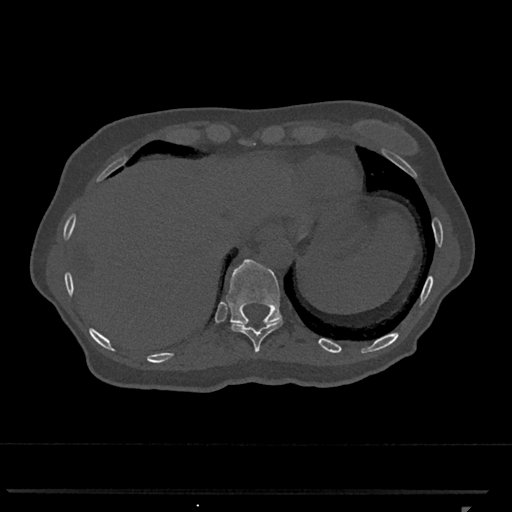
CT including the spine, one axial slice. Slice 545 of 793 in the series (ordered by position). Reconstruction kernel Br40s/3. 120 kVp. Bone window (W 1800 / L 400 HU). 0.5 mm slice thickness. 512 × 512 image matrix, field of view 380 × 380 mm. Patient: female, 62 years. Case-level facts recorded for this patient, not image findings: primary cancer: renal.
Annotated regions visible in this slice (semi-automatically segmented with operator editing):
- T10 vertebra: bounding box <230,321,283,353> (left, top, right, bottom; pixels)
- T11 vertebra: <226,259,282,327>